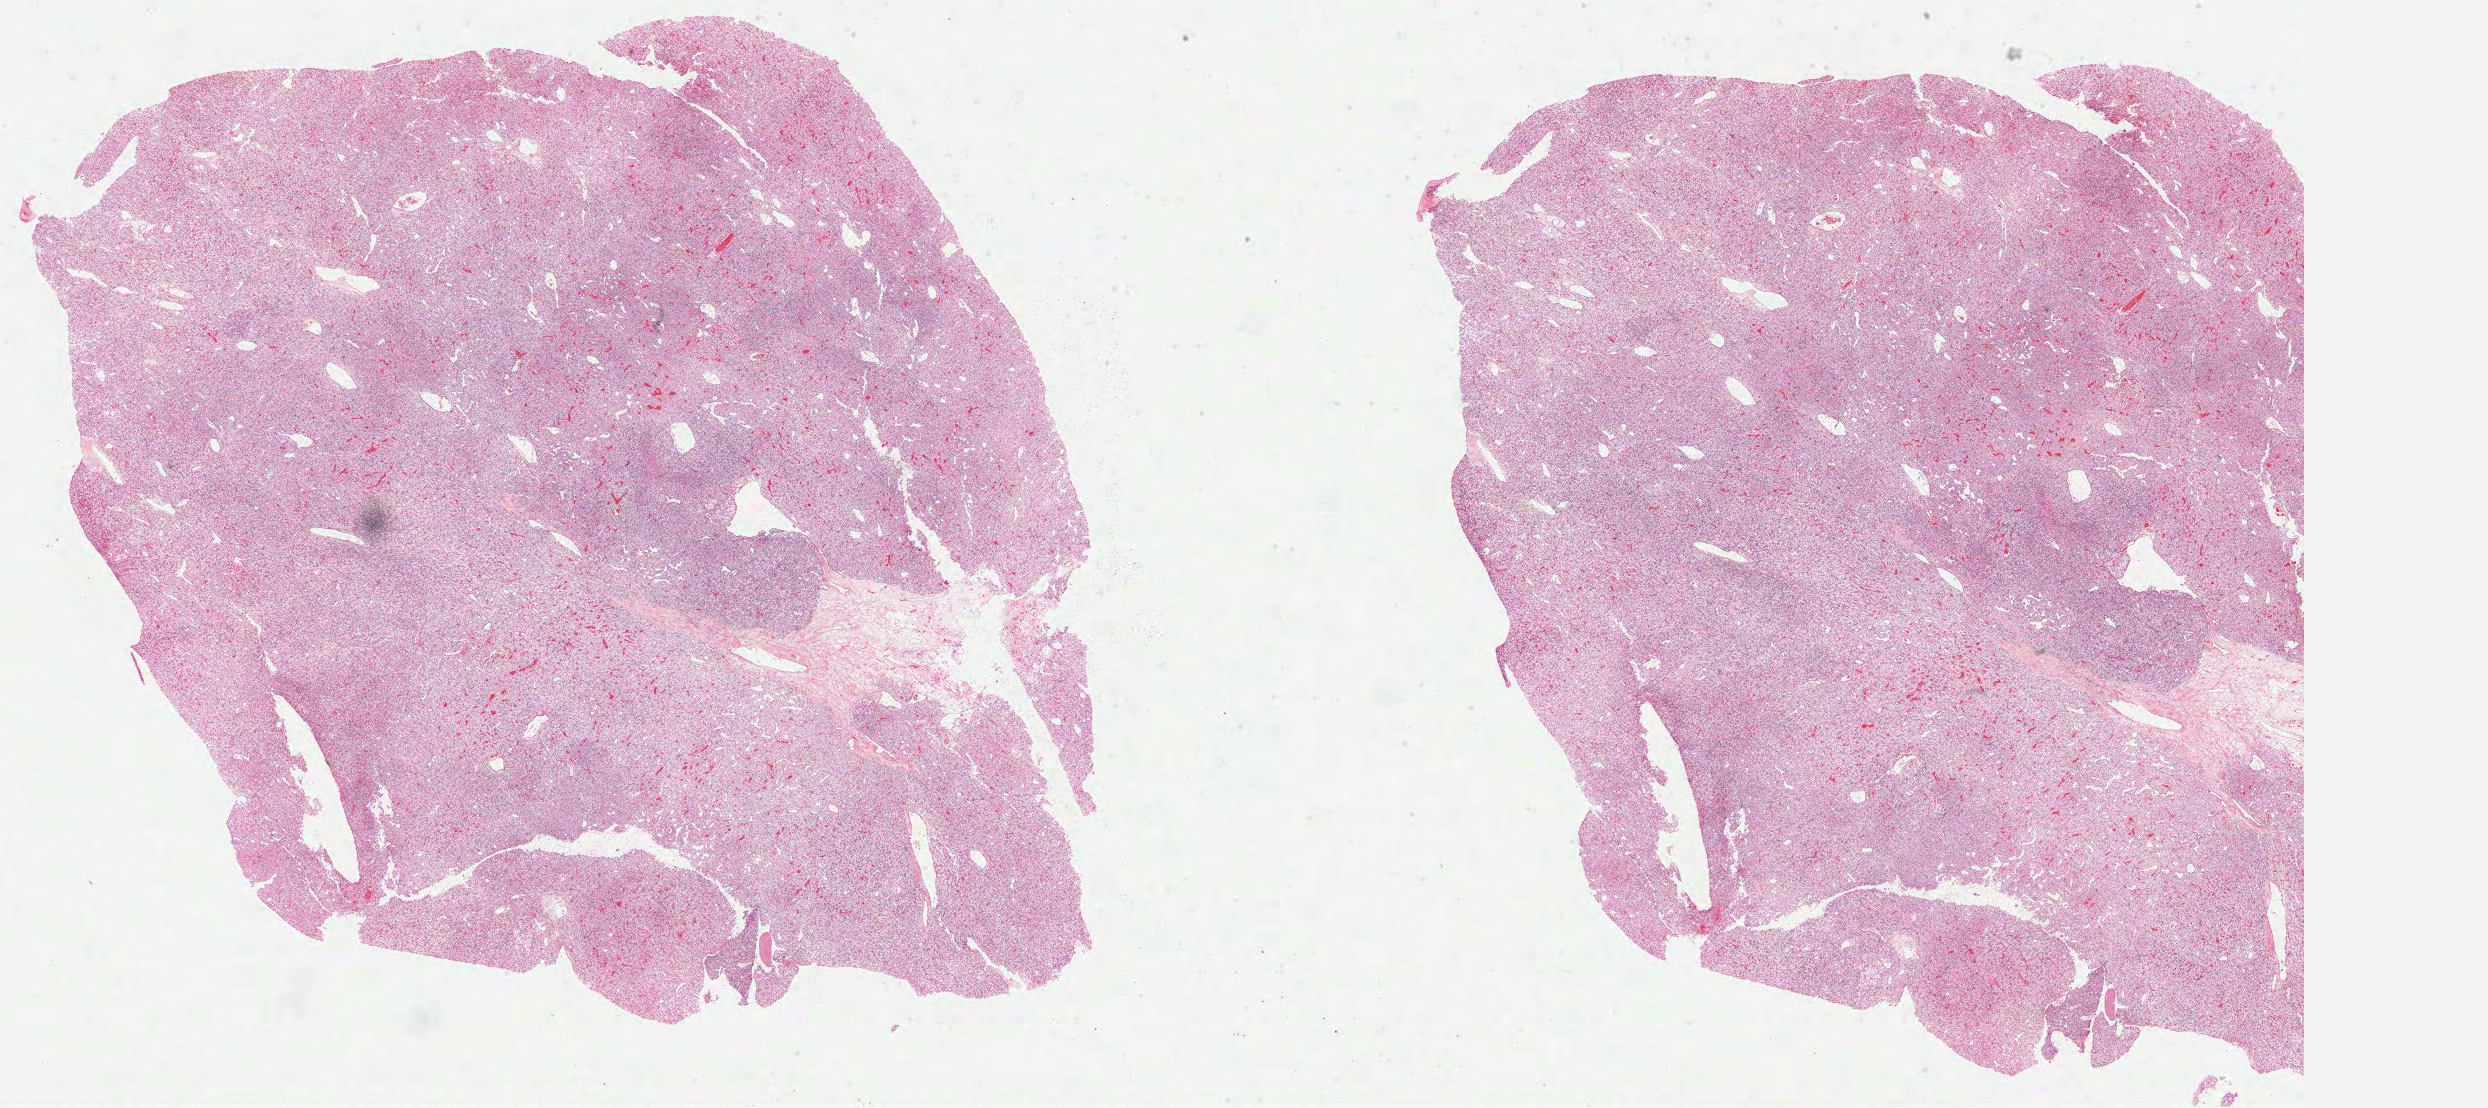
H&E-stained whole-slide image, whole scanned area (about 40.1 x 17.9 mm) shown as a low-resolution overview; FFPE section; kidney, primary tumour sample. Patient: male, age at initial diagnosis 74 years. Histologic grade: G3 (poorly differentiated).
Histologic diagnosis: Clear cell adenocarcinoma, NOS. AJCC pathologic stage: III (7th edition).